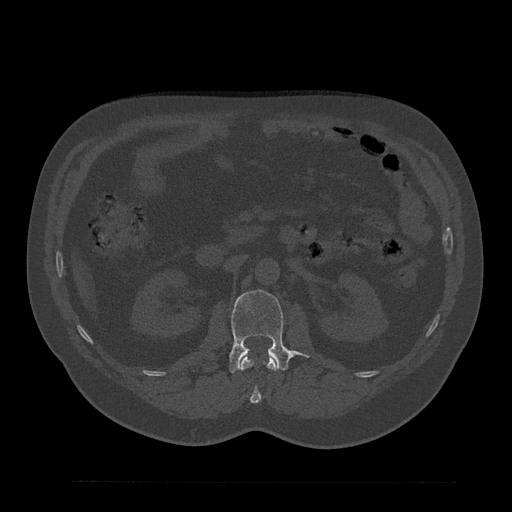
CT including the spine, one axial slice; bone window (W 1800 / L 400 HU); 512 × 512 image matrix, field of view 430 × 430 mm. Male patient, age 61 years. From the clinical record (not read from this slice): primary cancer: prostate.
Outlined on this slice (semi-automatic segmentation, software-assisted and operator-edited):
- L1 vertebra: bounding box [x1, y1, x2, y2] px = [240, 354, 278, 403]
- L2 vertebra: [229, 290, 301, 373]